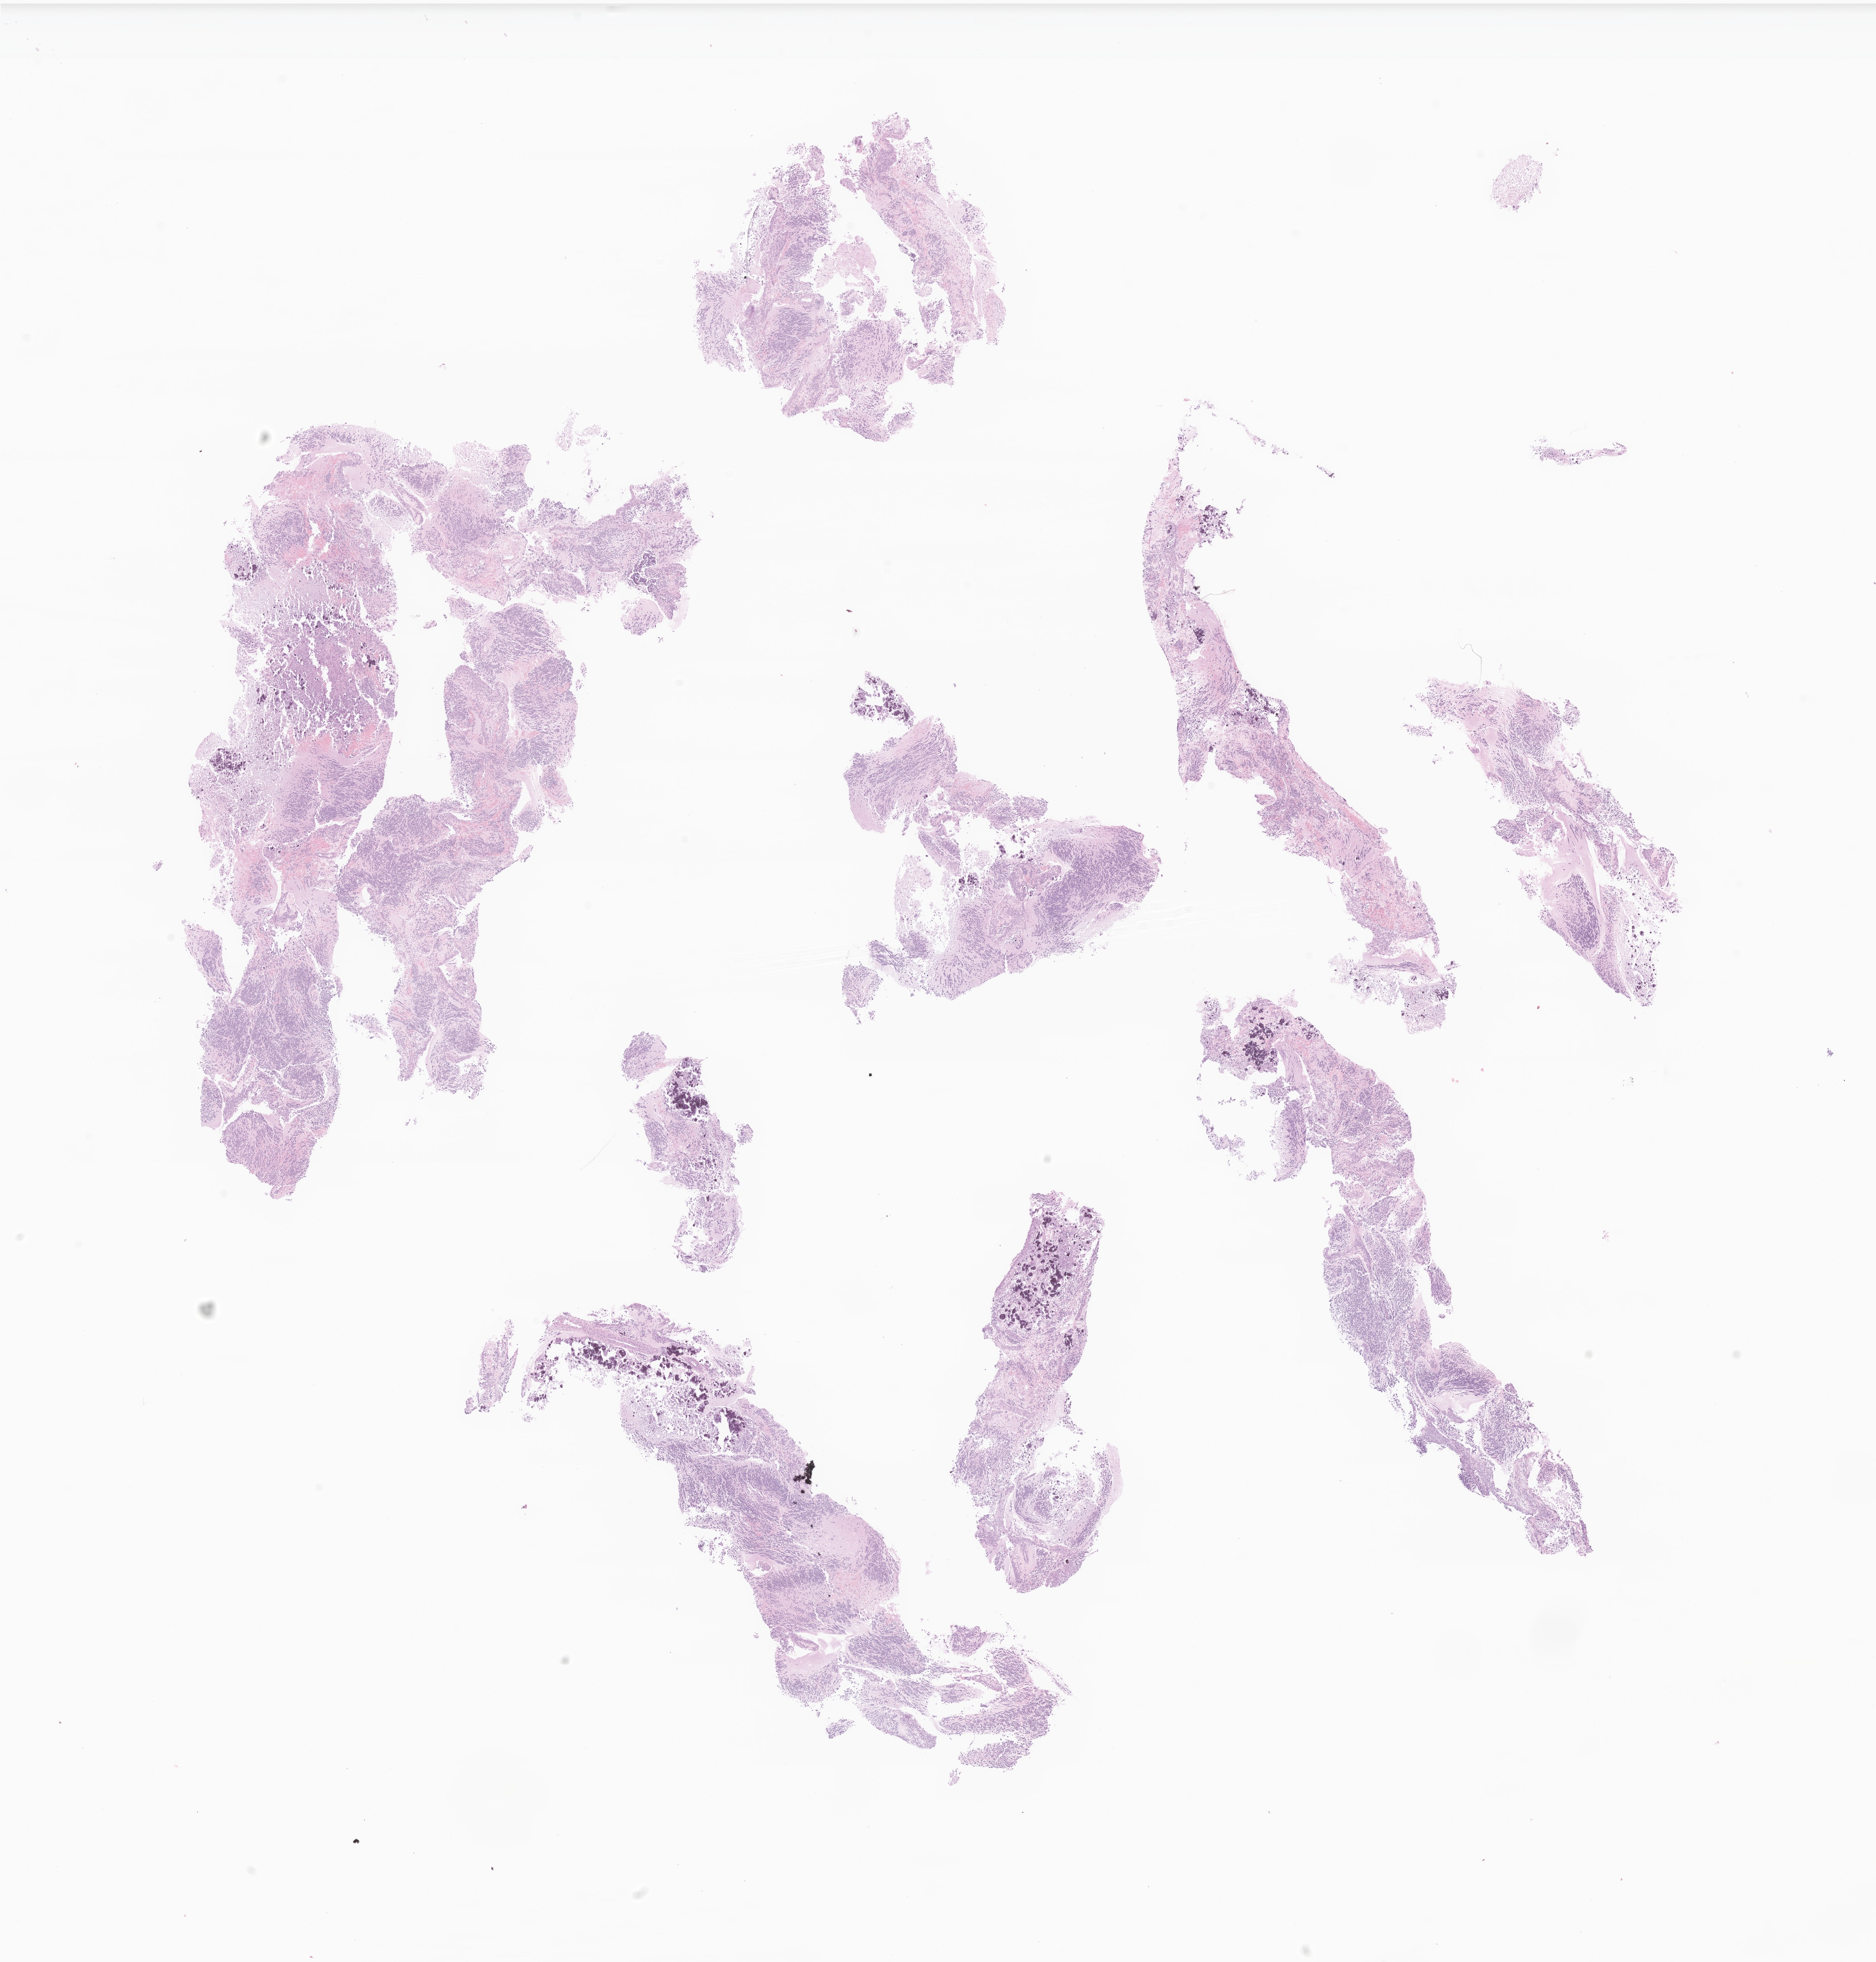
Digitized hematoxylin and eosin (H&E)-stained section of tumor tissue from the abdomen — shown as a low-resolution overview of the whole scanned area (about 20.0 x 20.9 mm); formalin-fixed paraffin-embedded section. Patient: male, age 291 days.
* recorded diagnosis: Neuroblastoma, NOS